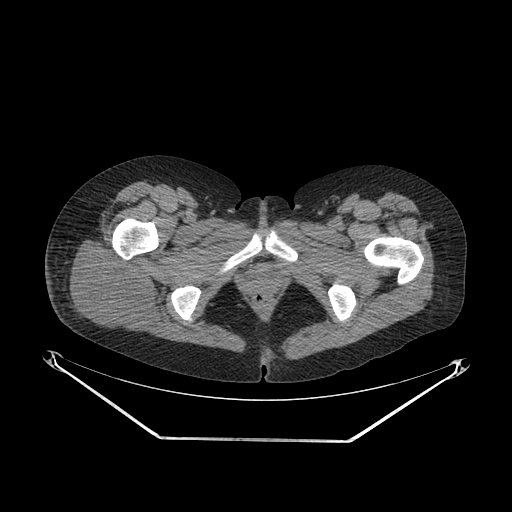
CT of an extremity soft-tissue mass (from a PET/CT study), one axial slice. Position 39 of 267 along the scan axis. 140 kVp. Soft-tissue window (W 400 / L 40 HU). 3.75 mm slice thickness. 512 × 512 image matrix, field of view 500 × 500 mm. Female patient. Case-level facts recorded for this patient, not image findings: histological type: epithelioid sarcoma with vascular differentiation; site of the primary tumour: right buttock.
Outlined on this slice (expert contour drawn on MRI and transferred to this co-registered scan by the dataset authors):
- gross tumour volume (mass): bounding box (x1, y1, x2, y2) in pixels: (66, 238, 156, 330)